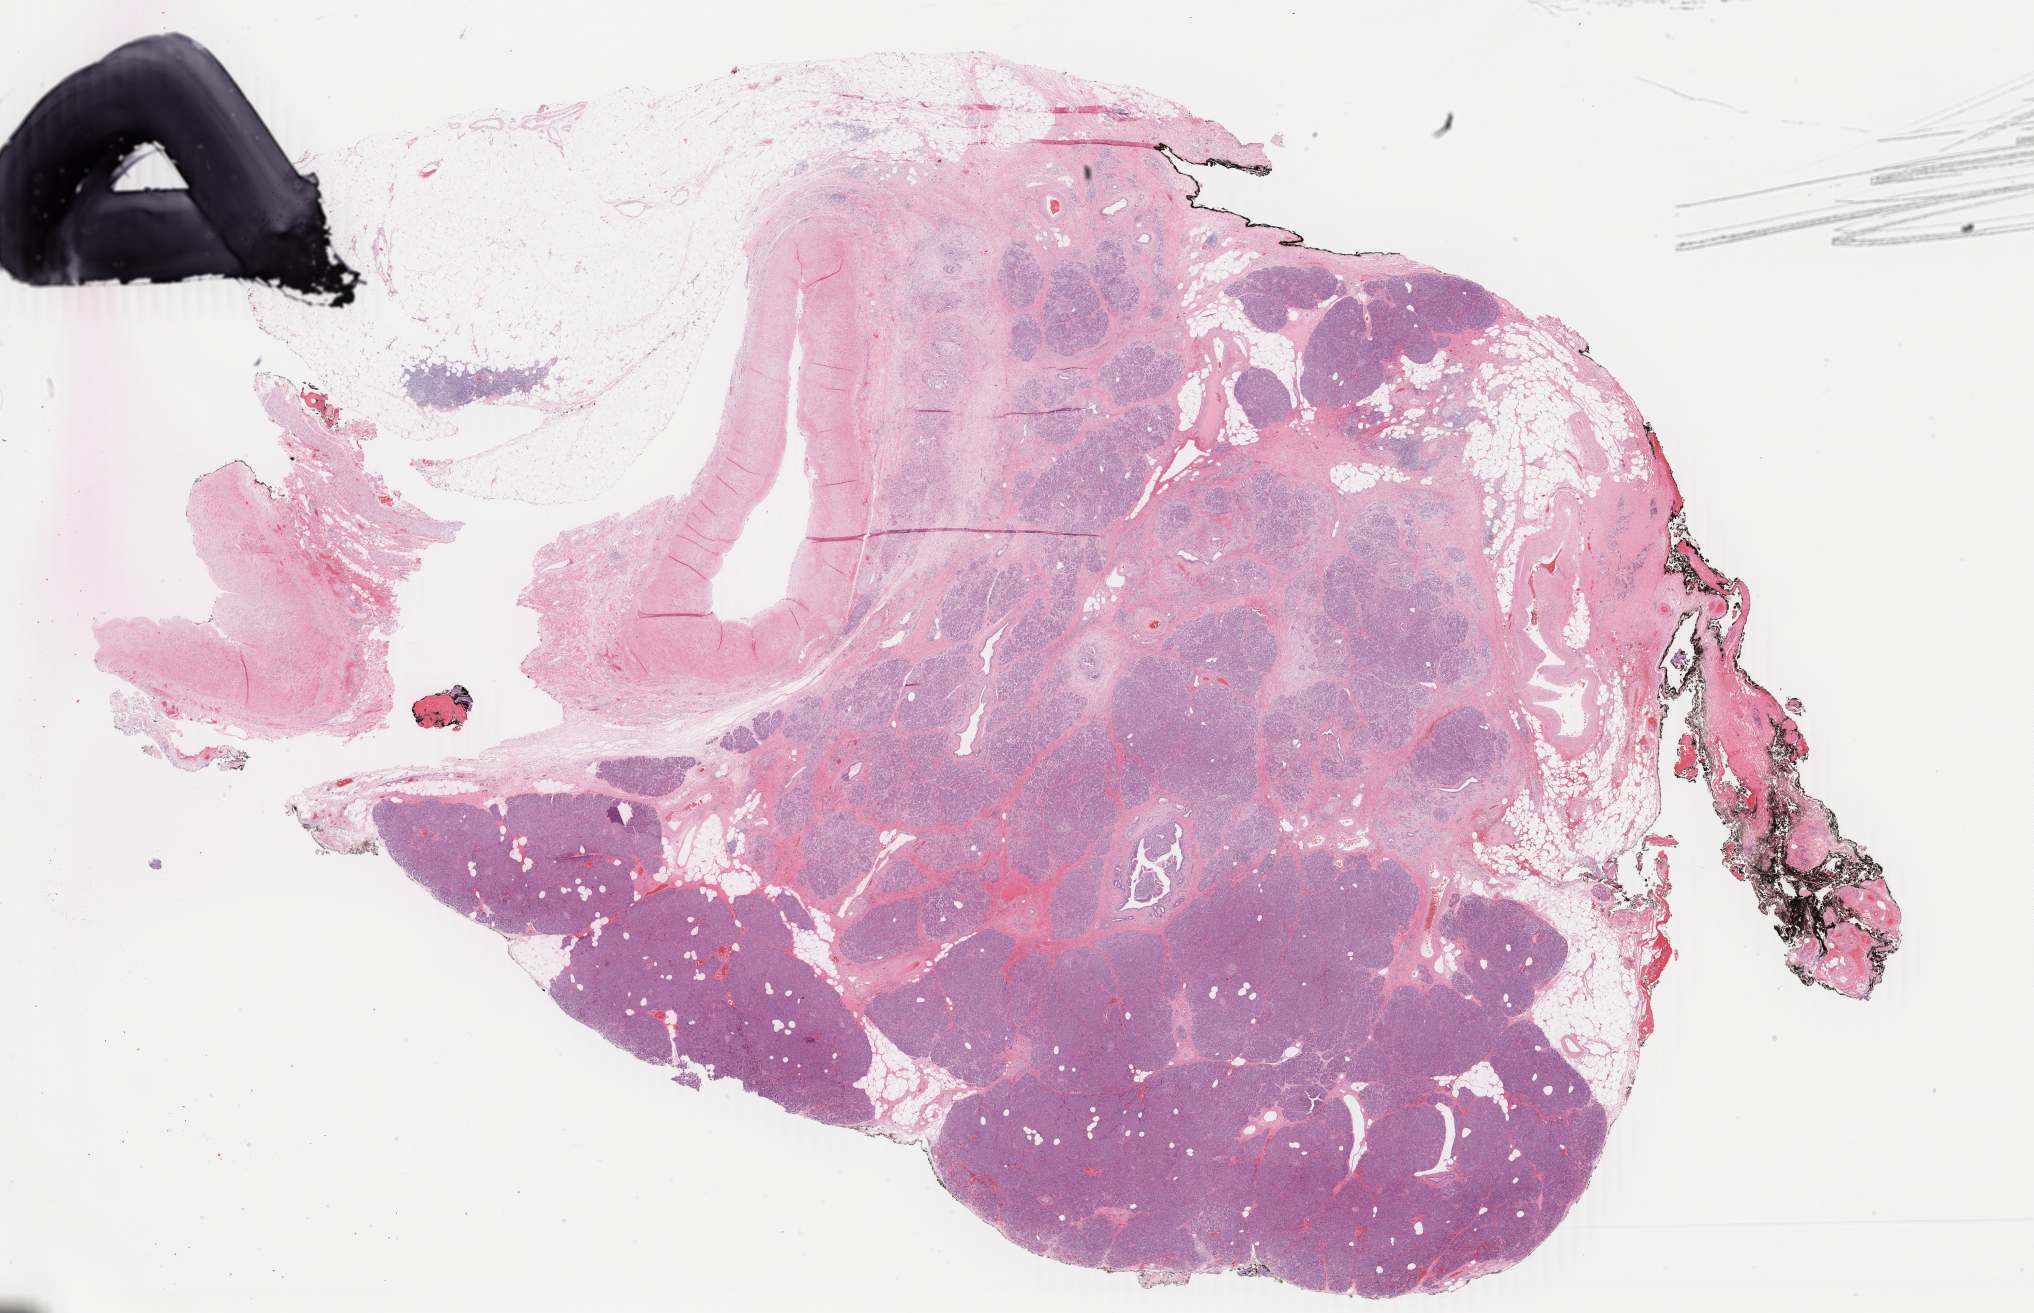
Whole-slide histology image, H&E — low-resolution overview of the scanned area, about 32.4 x 20.9 mm, formalin-fixed paraffin-embedded (FFPE) diagnostic section, pancreas, primary tumour sample. Patient: female, age at initial diagnosis 66 years. Histologic grade: G2 (moderately differentiated).
Diagnosis: Infiltrating duct carcinoma, NOS. AJCC pathologic stage: IV.